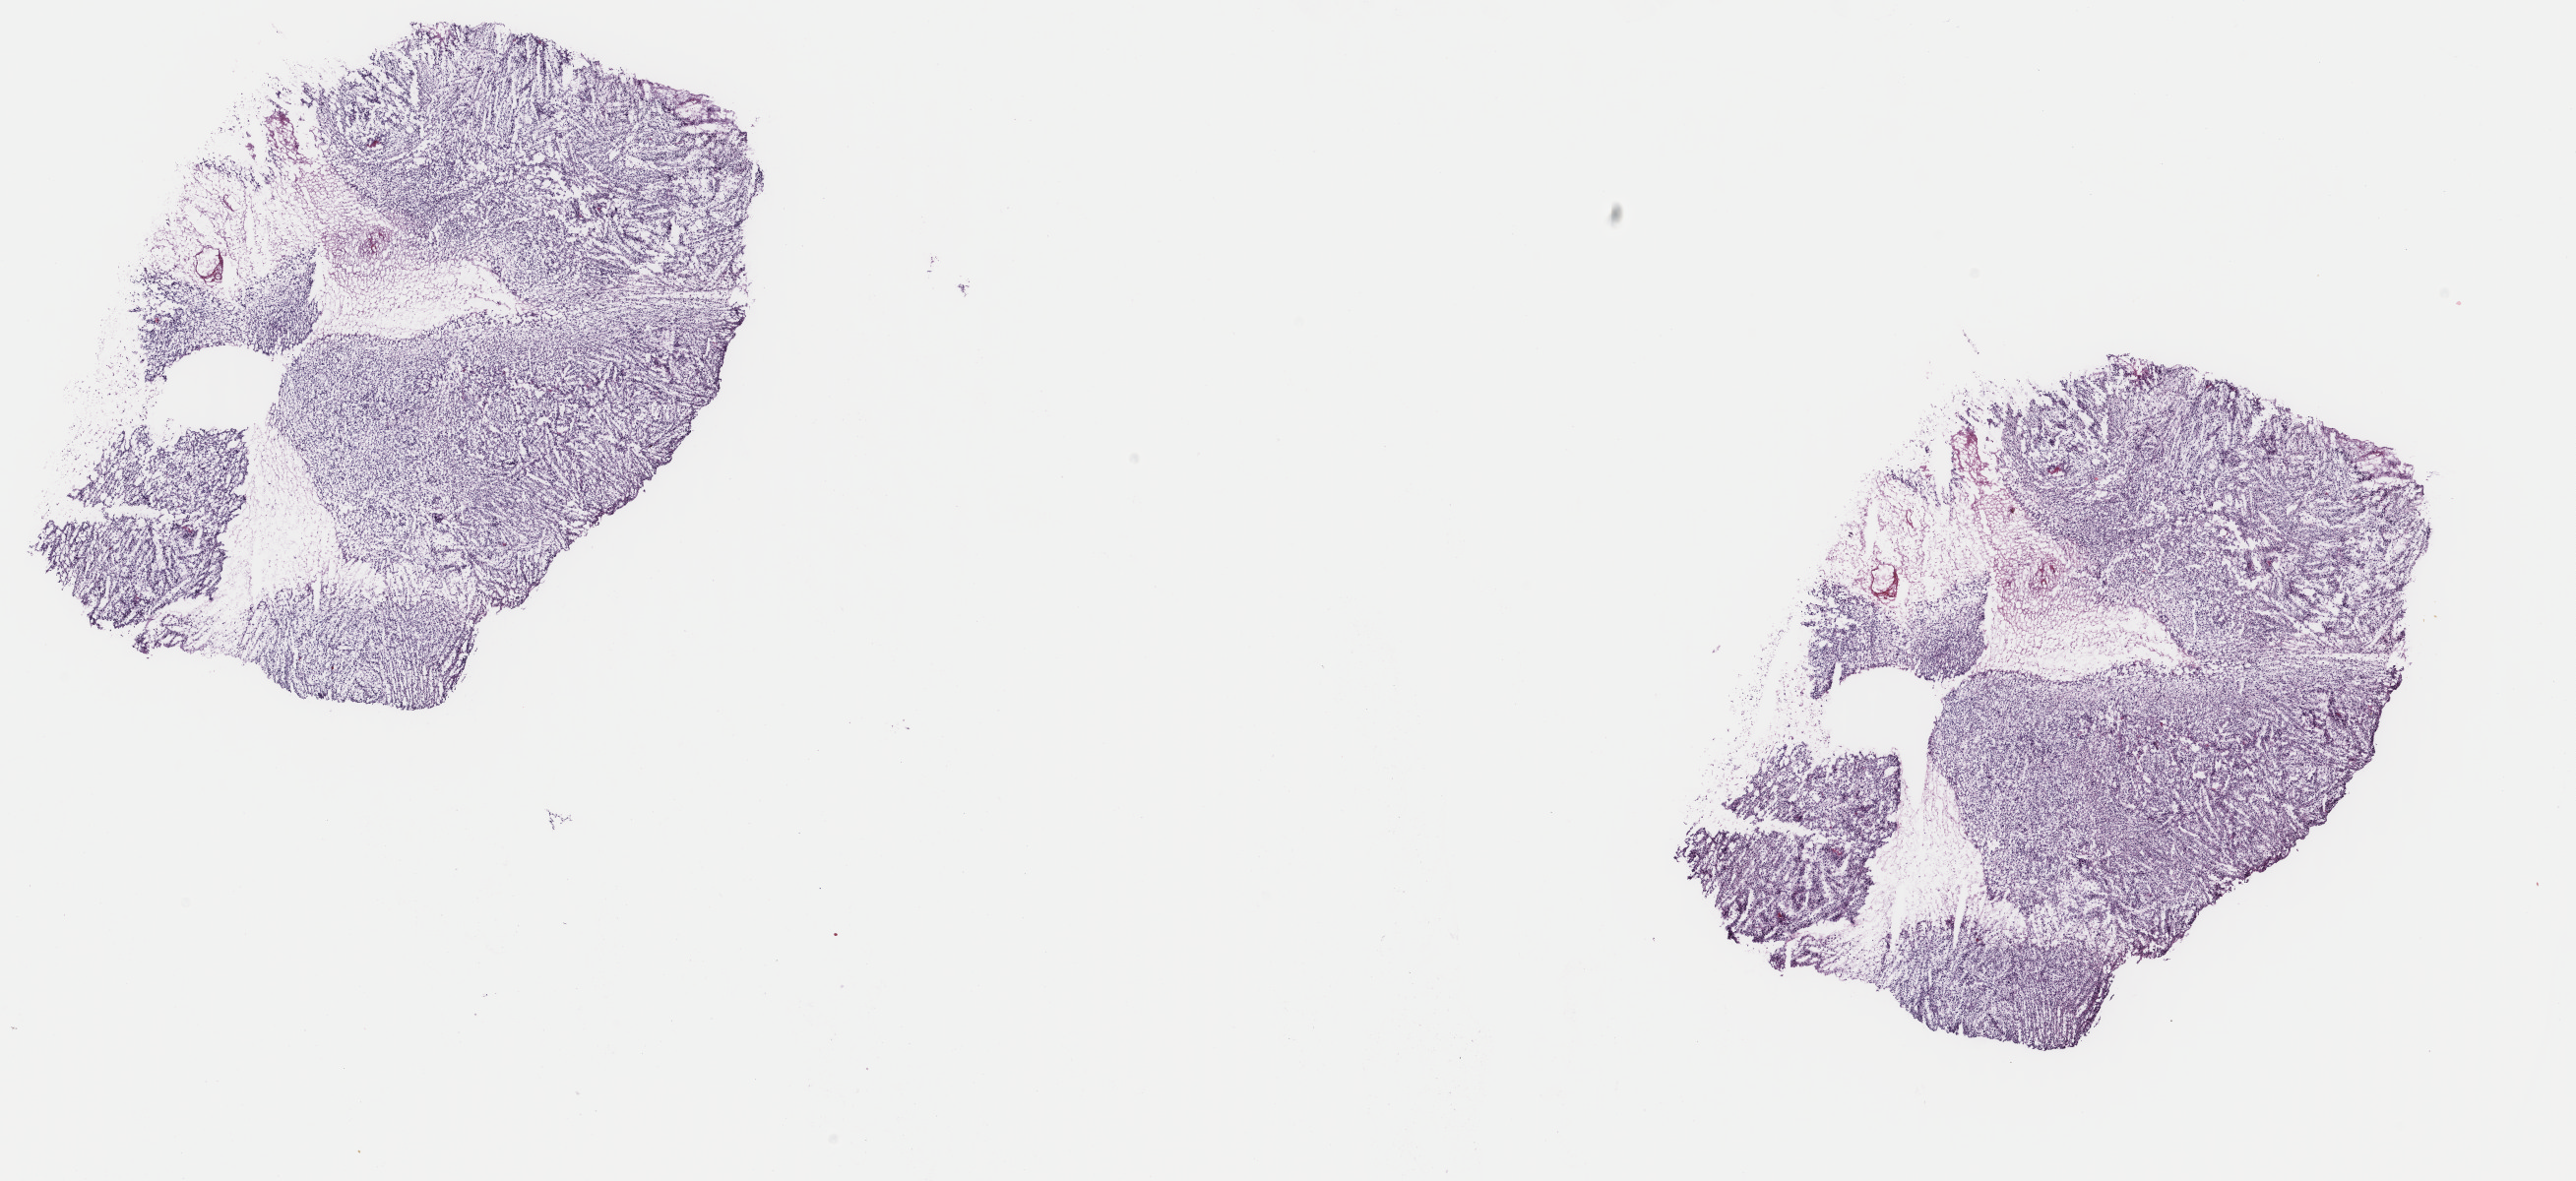
Whole-slide histology image, H&E-stained — a low-resolution overview of the entire scanned area, about 20.8 x 9.5 mm, frozen section from the top of the tissue portion, primary tumour sample from the retroperitoneum and peritoneum. Patient: female, age at initial diagnosis 44 years.
Diagnosis: Dedifferentiated liposarcoma.